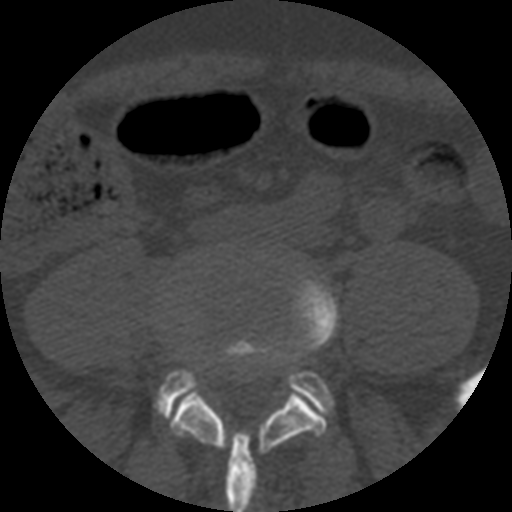
CT including the spine, one axial slice. Slice 80 of 508 in the series (ordered by position). Reconstruction kernel STANDARD. 120 kVp. Bone window (W 1800 / L 400 HU). 512 × 512 image matrix, field of view 160 × 160 mm. Patient age 57 years. Case-level facts recorded for this patient, not image findings: primary cancer: prostate.
Annotated regions visible in this slice (semi-automatic segmentation, software-assisted and operator-edited):
- L4 vertebra: bounding box [x1, y1, x2, y2] px = [161, 274, 339, 512]
- L5 vertebra: [156, 370, 332, 417]